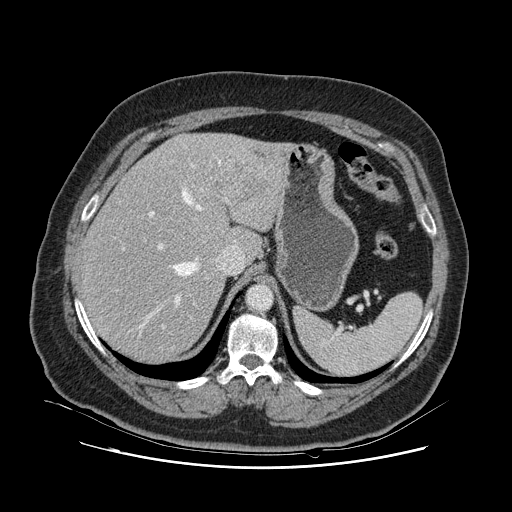
Contrast-enhanced abdominal CT, one axial slice. Position 85 of 132 along the scan axis. Intravenous contrast given. Soft-tissue window (W 400 / L 40 HU). 2.5 mm slice thickness. 512 × 512 image matrix. Female patient, age 73 years. From the clinical record (not read from this slice): diagnosis: colorectal cancer liver metastases, imaged before liver resection; multiple liver metastases: no; largest metastasis: 7 cm; disease in both lobes: no.
Structures marked on this image (manually delineated by an expert):
- hepatic veins: bounding box [x1, y1, x2, y2] px = [138, 155, 235, 334]
- liver: [82, 133, 287, 363]
- planned liver remnant (the part of the liver to remain after resection): [82, 160, 244, 363]
- portal vein (with intrahepatic branches): [122, 164, 228, 328]
- liver metastasis: [238, 171, 266, 197]